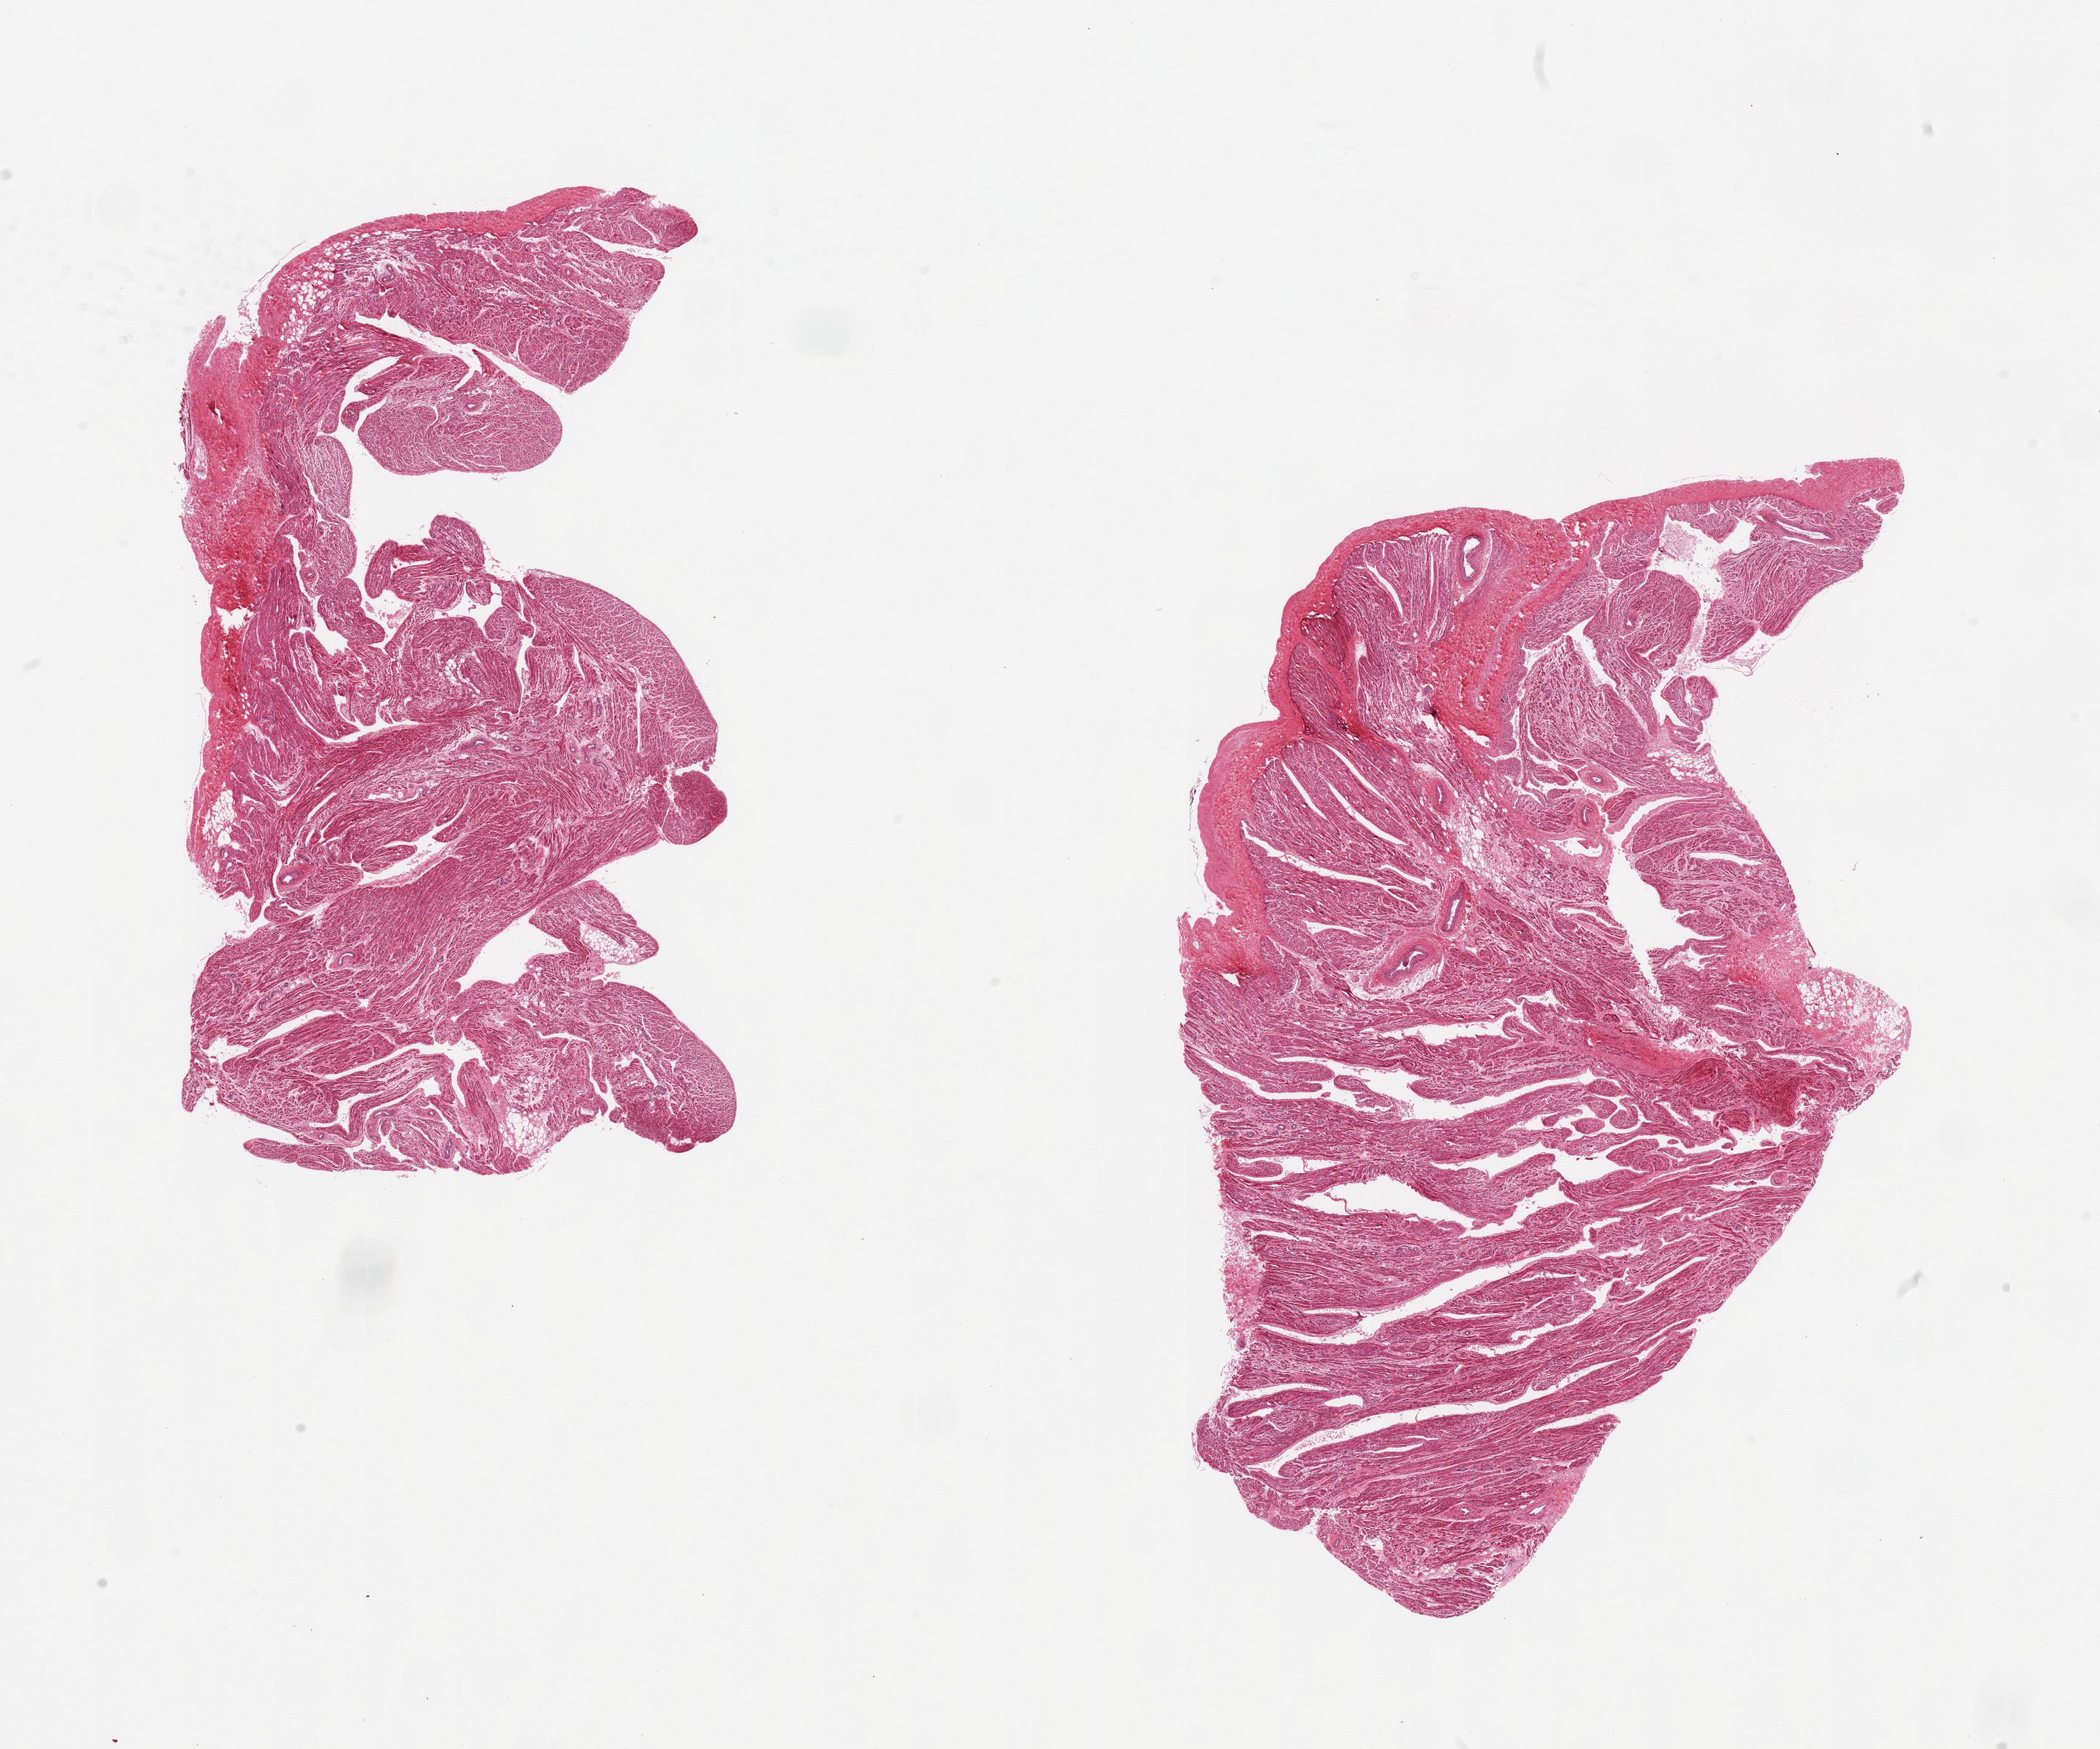
Hematoxylin and eosin (H&E) whole-slide image, shown as a low-resolution overview of the whole scanned area (about 22.6 x 18.9 mm); PAXgene-fixed paraffin-embedded (PFPE) section; sampled site (target tissue): auricular appendage; tissue donor sample.
Pathologist's review note for this sample: 2 pieces; <5% extraneous fibrofatty tissue.